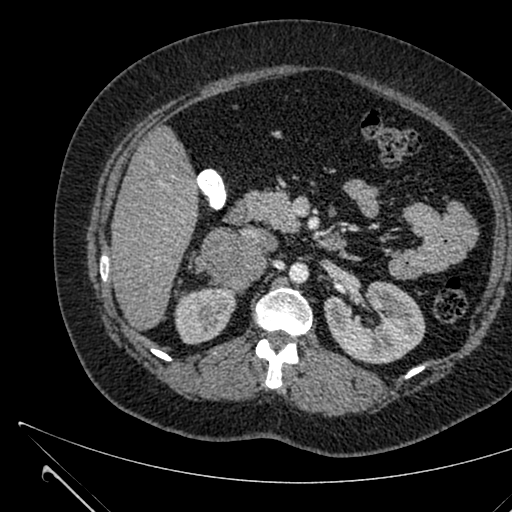
Contrast-enhanced abdominal CT, one axial slice. Position 367 of 731 along the scan axis. 120 kVp. Intravenous contrast given. Soft-tissue window (W 400 / L 40 HU). 512 × 512 image matrix, field of view 376 × 376 mm. Patient: female, 36 years. From the clinical record (not read from this slice): diagnosis: adrenocortical carcinoma; tumour side: right adrenal; tumour size at pathology: 10 cm; Ki-67 index: 20 %; stage (as recorded): 4.
Annotated regions visible in this slice (semi-automatically segmented with operator editing):
- mass: bounding box (x1, y1, x2, y2) in pixels: (201, 228, 264, 291)